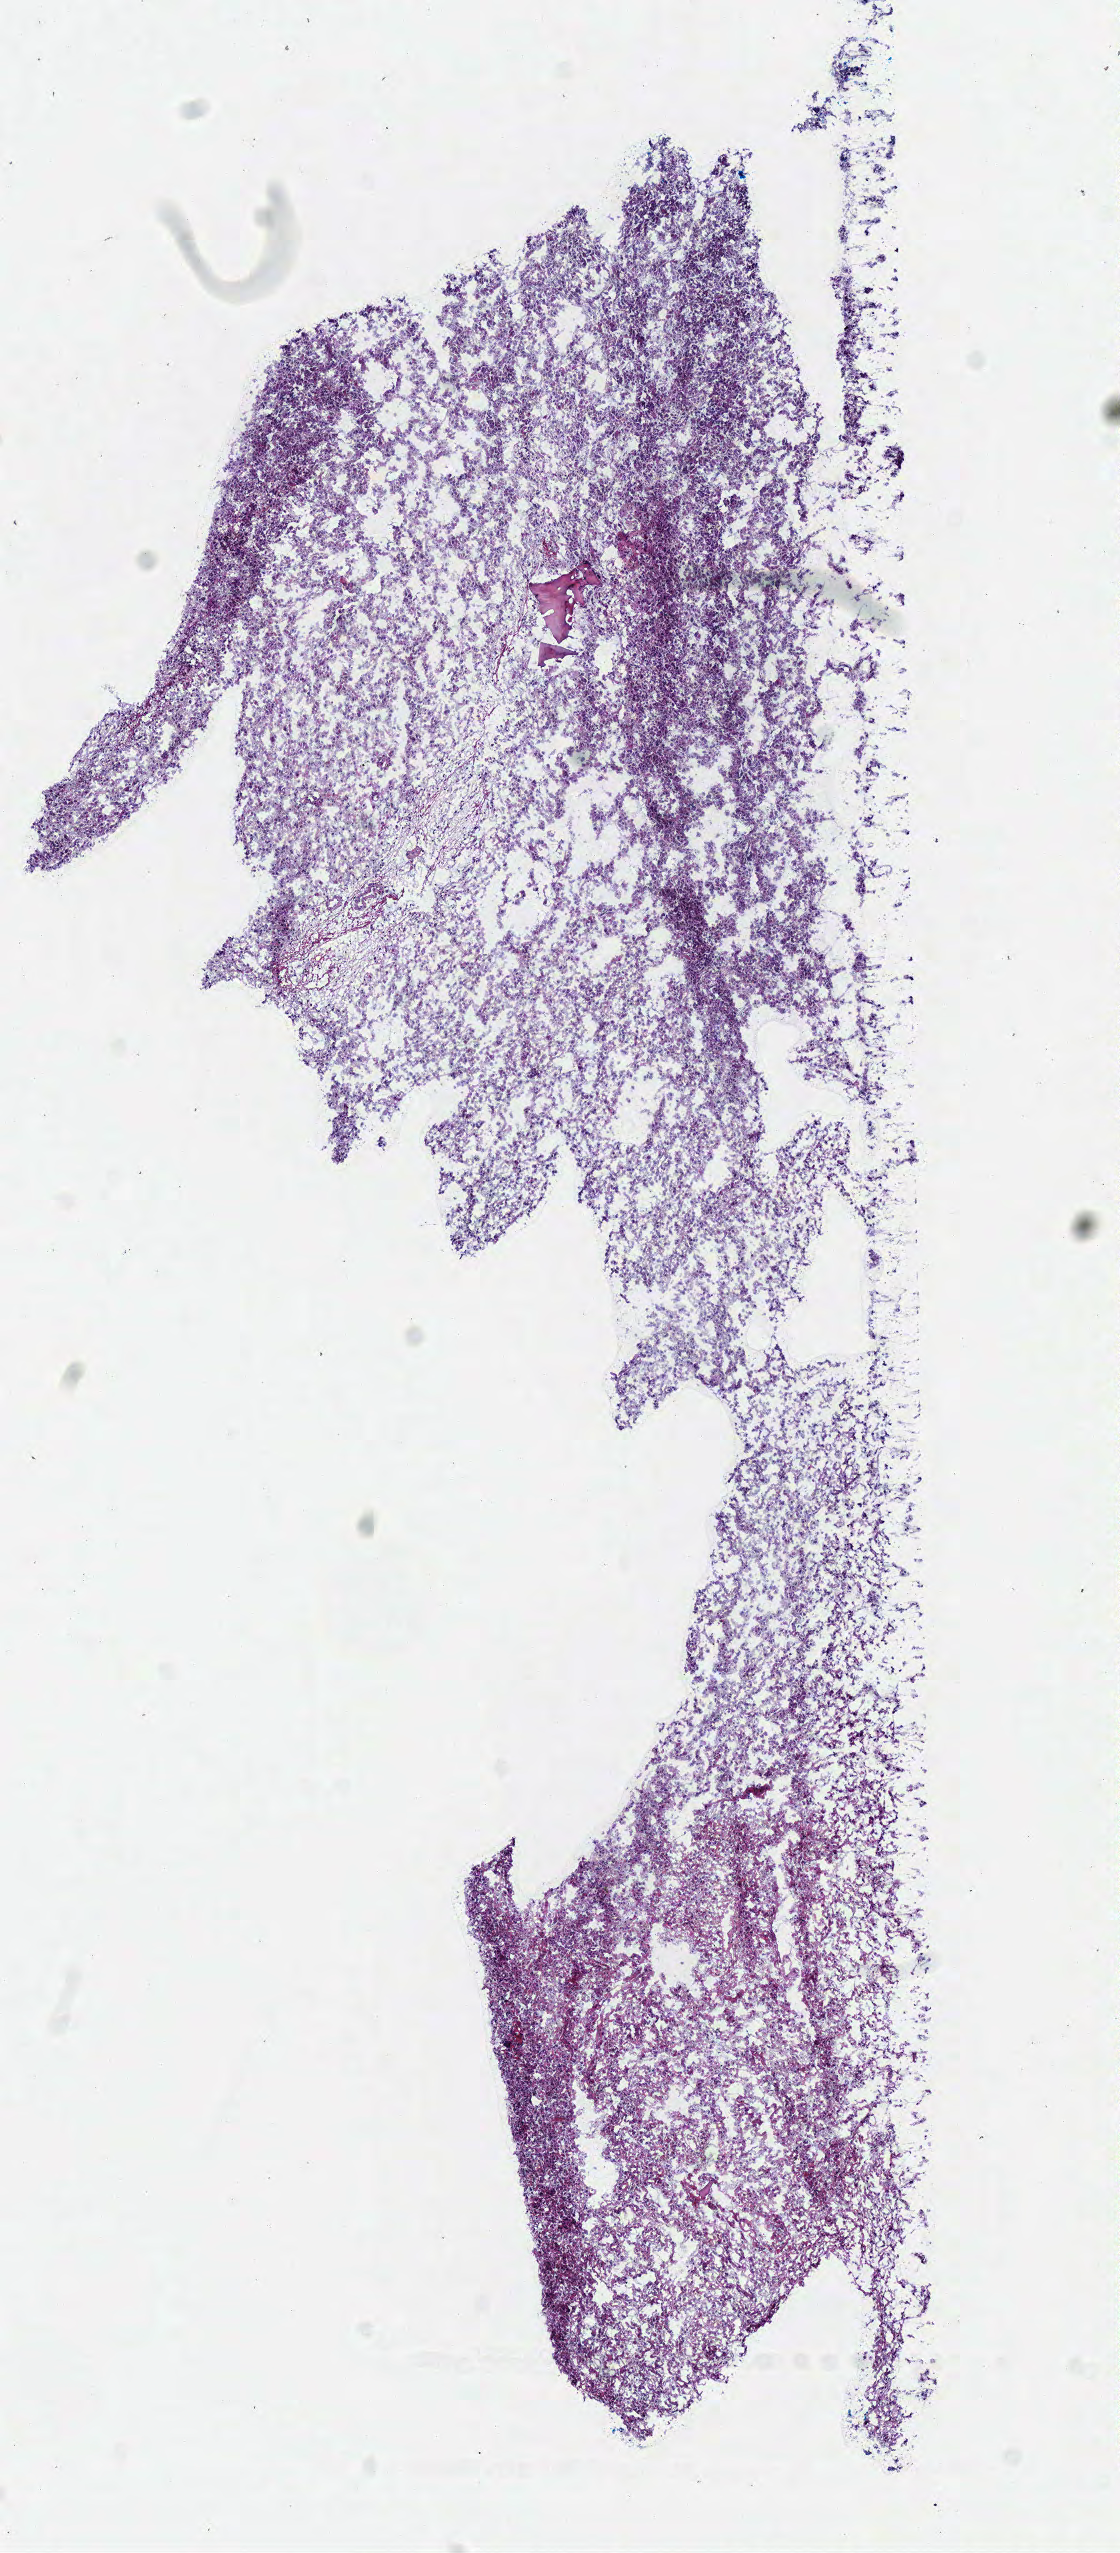
Digitized H&E-stained tissue section (whole slide) — shown as a low-resolution overview of the whole scanned area (about 4.4 x 10.0 mm), frozen section from the bottom of the tissue portion, brain, primary tumour sample. Female, age 23 years at initial diagnosis. Histologic grade: G2 (moderately differentiated). Slide review estimates, as recorded: tumour cells 100%, tumour nuclei 80%, normal cells 0%, stromal cells 0%, necrosis 0%.
Diagnosis: Astrocytoma, NOS (cerebrum).